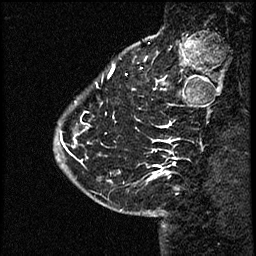
Breast MRI (dynamic contrast-enhanced), one sagittal slice; dynamic contrast-enhanced study with each time point stored as its own series, time point 2 of 4 at this slice position (early post-contrast, ordered by acquisition time); 1.5 T; TE 4.2 ms, TR 17.6 ms; 2 mm slice thickness; 256 × 256 image matrix, field of view 200 × 200 mm. Patient: female, 43 years. From the clinical record (not read from this slice): setting: breast cancer imaged before/during neoadjuvant chemotherapy.
Outlined on this slice (semi-automatic segmentation, software-assisted and operator-edited):
- analysis volume of interest (the breast-tissue region the enhancement analysis was run in; not a lesion): box from (x=60, y=56) to (x=169, y=191) px
- tumour enhancement mask (voxels above the 100 % enhancement threshold inside the analysis volume of interest): (x=63, y=143)–(x=167, y=173)